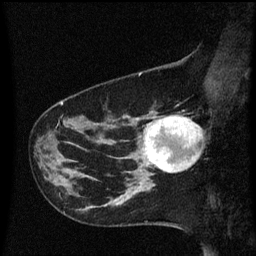
Breast MRI (dynamic contrast-enhanced), one sagittal slice. Position 19 of 60 along the scan axis. Dynamic contrast-enhanced series, image 2 of 3 at this slice position (ordered by acquisition). 1.5 T. TE 4.2 ms, TR 8.4 ms. 2 mm slice thickness. 256 × 256 image matrix, field of view 200 × 200 mm. Female patient, age 41 years. From the clinical record (not read from this slice): setting: breast cancer imaged before/during neoadjuvant chemotherapy; receptor status: triple-negative.
Annotated regions visible in this slice (semi-automatically segmented with operator editing):
- analysis volume of interest (the breast-tissue region the enhancement analysis was run in; not a lesion): box from (x=138, y=112) to (x=201, y=177) px
- tumour enhancement mask (voxels above the 70 % enhancement threshold inside the analysis volume of interest): (x=145, y=116)–(x=200, y=173)